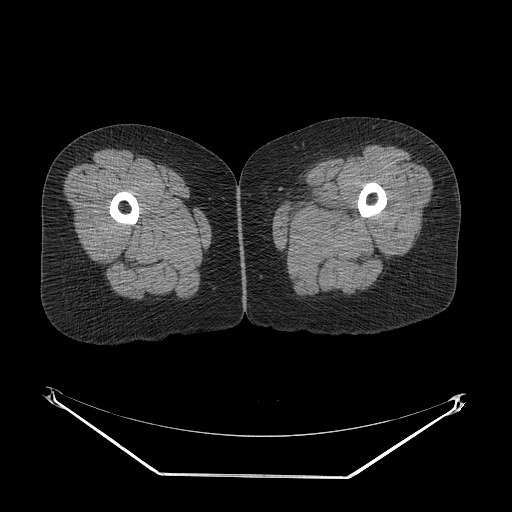
CT of an extremity soft-tissue mass (from a PET/CT study), one axial slice; position 4 of 267 along the scan axis; reconstruction kernel STANDARD; soft-tissue window (W 400 / L 40 HU); 512 × 512 image matrix, field of view 500 × 500 mm. Female patient. Case-level facts recorded for this patient, not image findings: histological type: myxofibrosarcoma; grade: intermediate; site of the primary tumour: left thigh.
Annotated regions visible in this slice (expert contour drawn on MRI and transferred to this co-registered scan by the dataset authors):
- gross tumour volume including surrounding oedema: bounding box <290,203,348,232> (left, top, right, bottom; pixels)